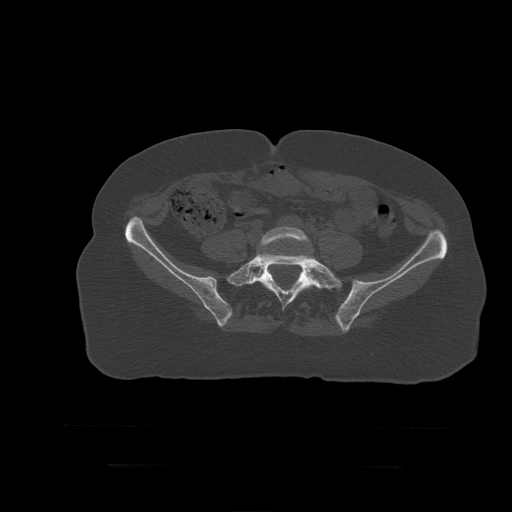
CT including the spine, one axial slice. Position 58 of 399 along the scan axis. Reconstruction kernel STANDARD. 120 kVp. Bone window (W 1800 / L 400 HU). 1.25 mm slice thickness. 512 × 512 image matrix, field of view 450 × 450 mm. Patient age 41 years. Case-level facts recorded for this patient, not image findings: primary cancer: breast.
Annotated regions visible in this slice (semi-automatic segmentation, software-assisted and operator-edited):
- L5 vertebra: bounding box <258,227,312,254> (left, top, right, bottom; pixels)